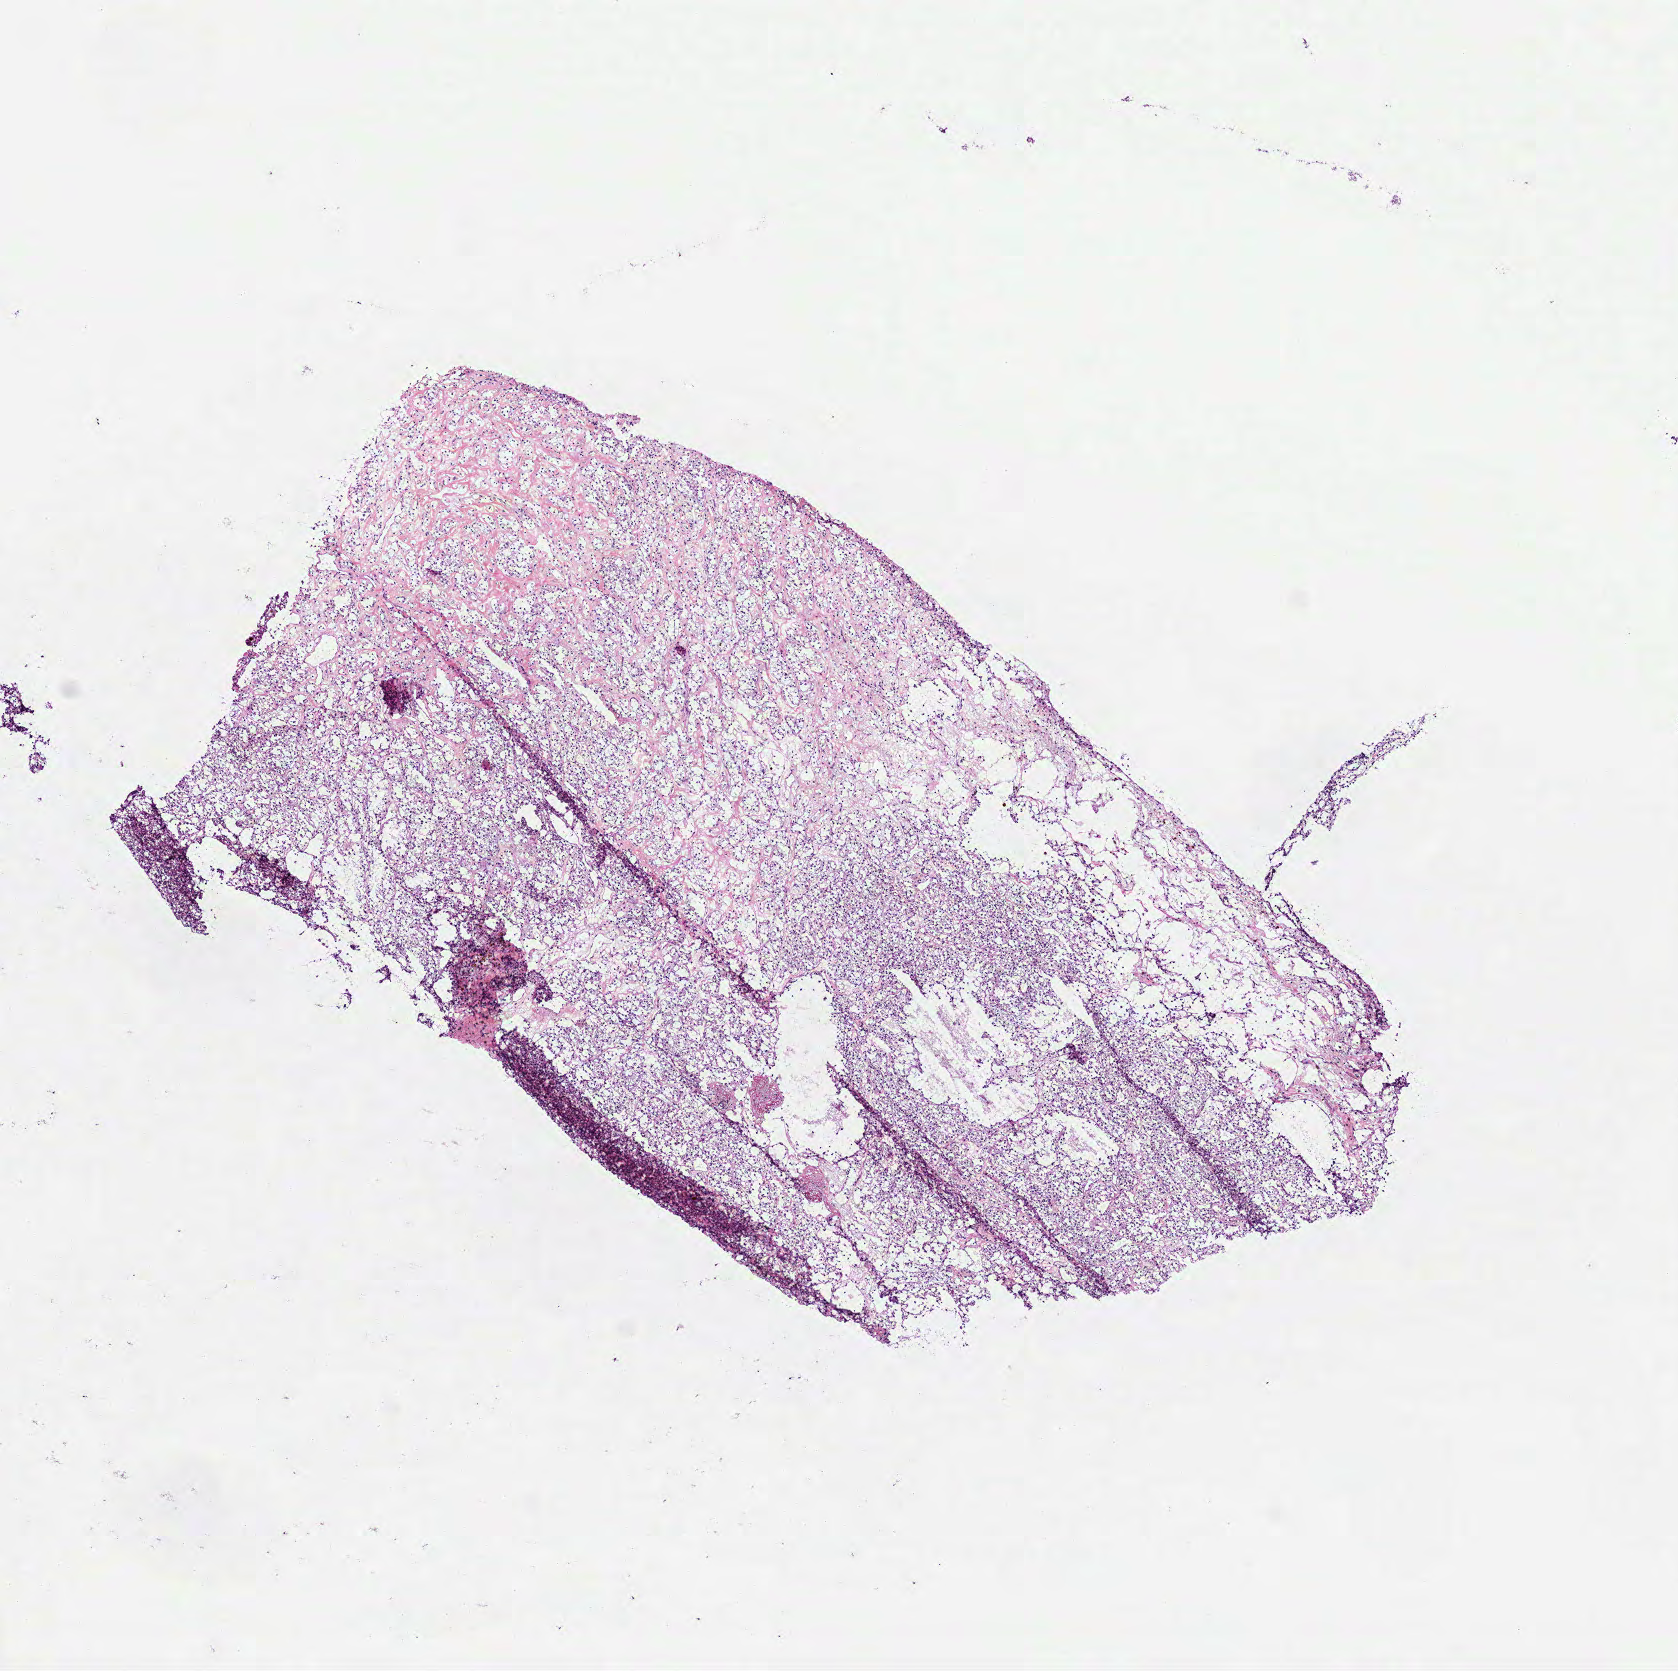
Hematoxylin and eosin (H&E) stained whole-slide image, a low-resolution overview of the entire scanned area, about 6.8 x 6.7 mm (slide scanned at 40x); frozen section from the bottom of the tissue portion; sample: primary tumour, kidney. Female patient; age at initial diagnosis 41 years. Histologic grade: G2 (moderately differentiated). Composition of this section per pathologist review: tumour cells 90%, tumour nuclei 85%, normal cells 0%, stromal cells 10%, necrosis 0%.
Laterality: right. TNM: T1b NX M0. Pathologic diagnosis: Clear cell adenocarcinoma, NOS. AJCC pathologic stage: I (6th edition).